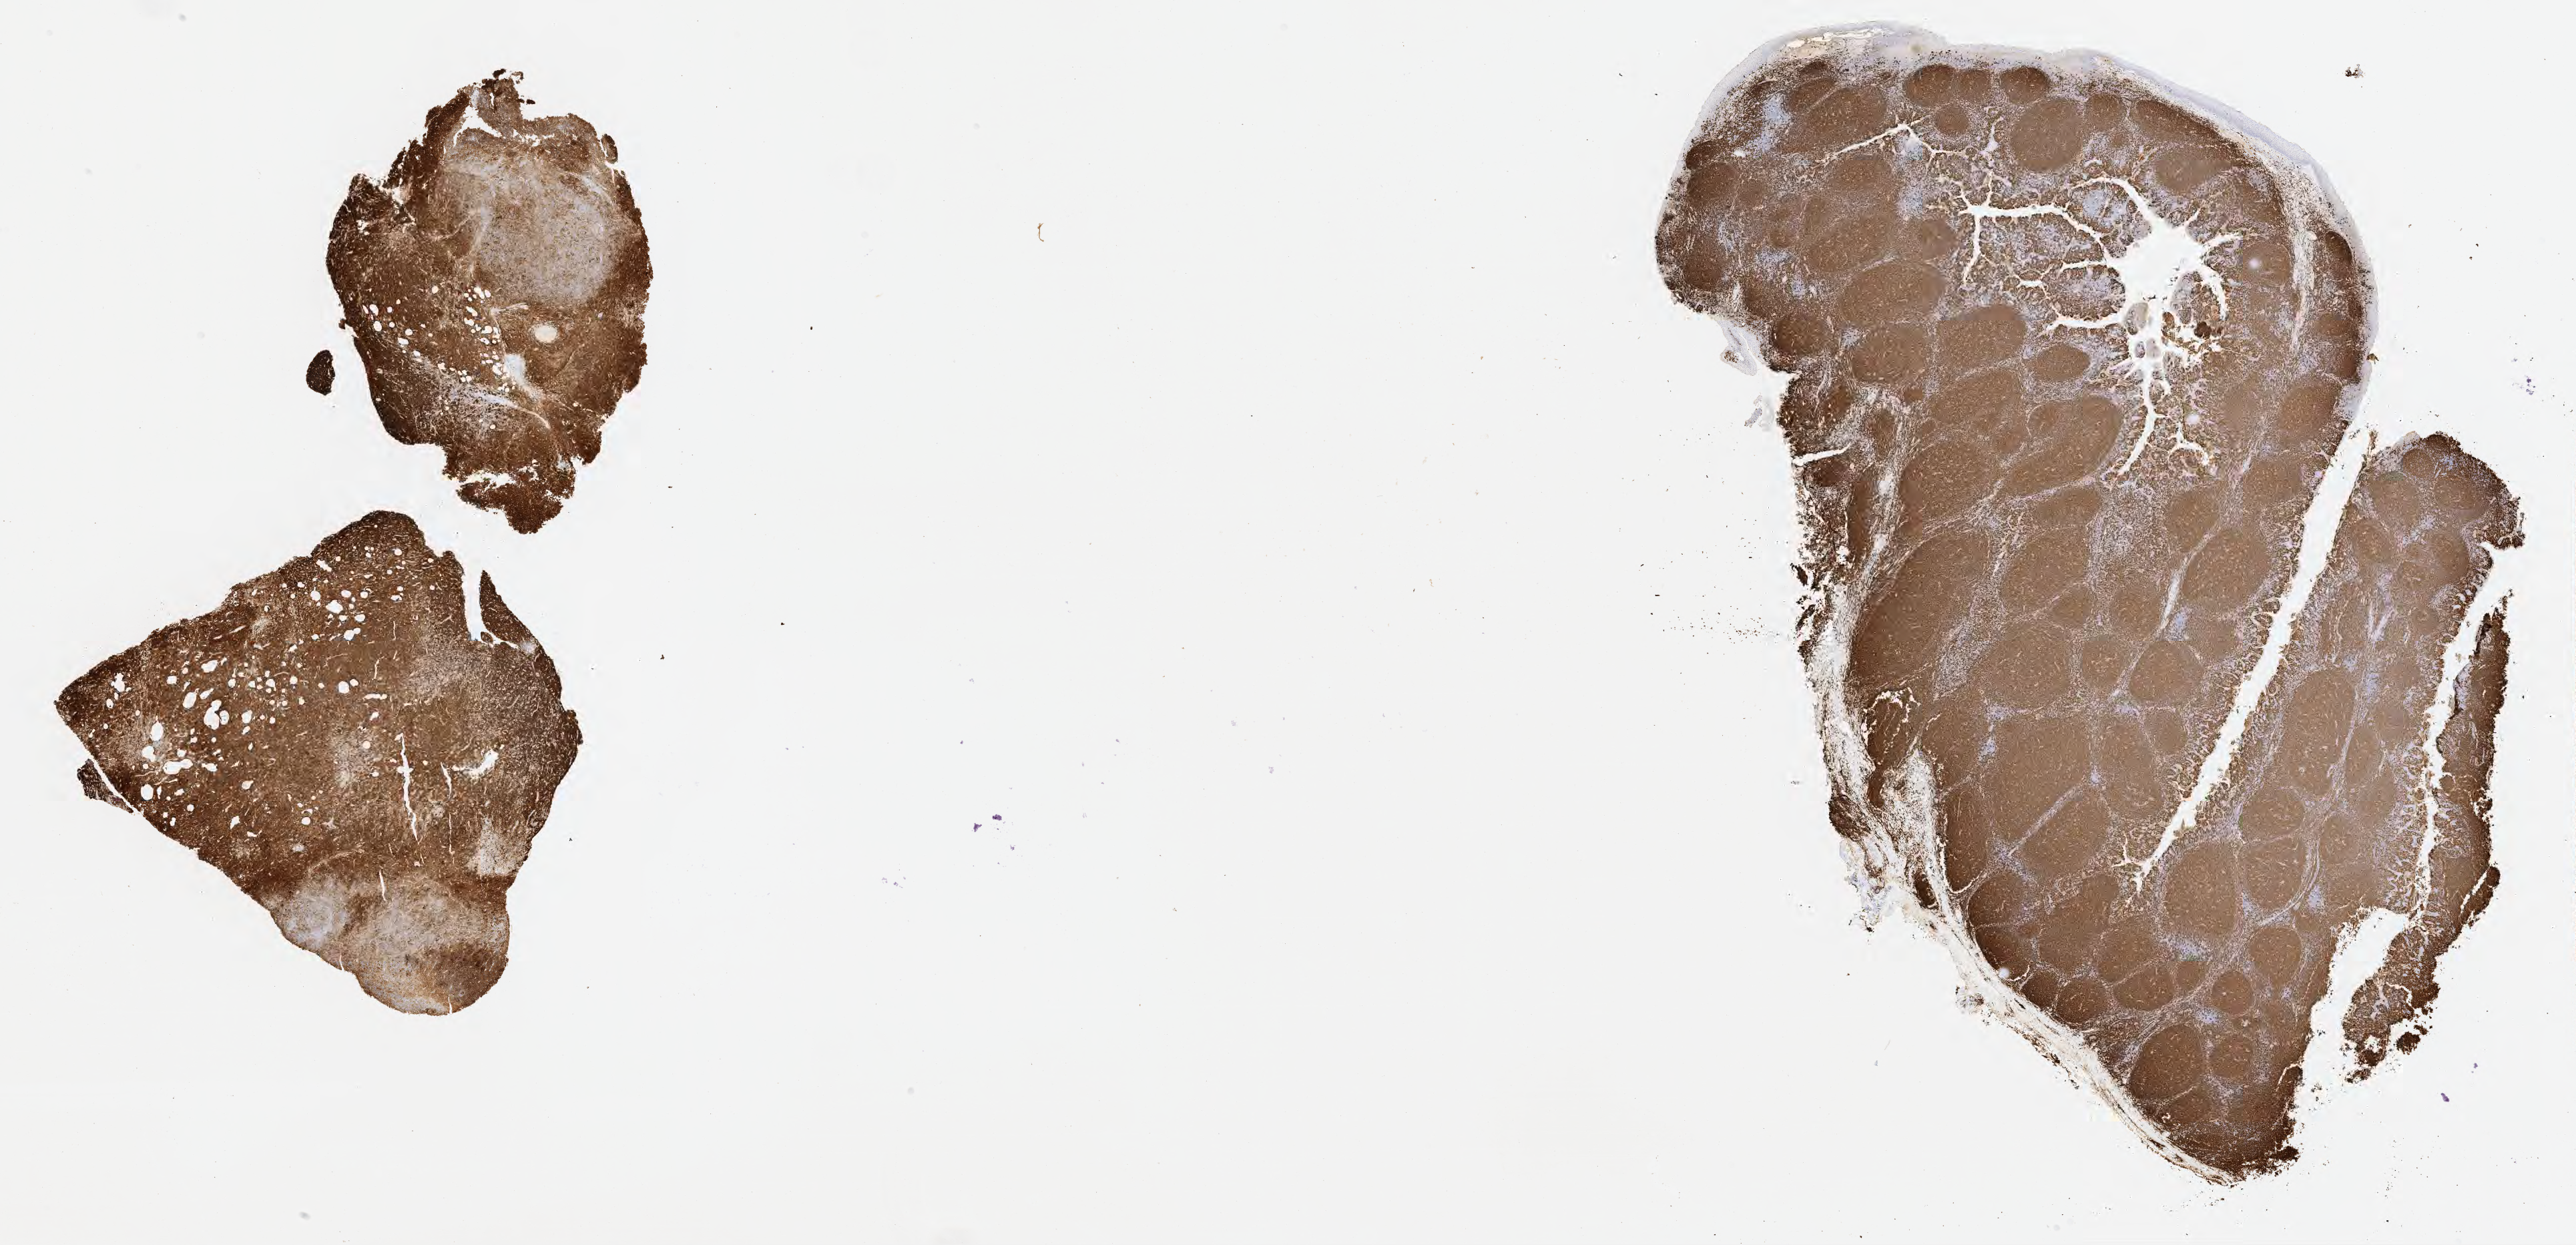
IHC for CD20, whole-slide image, a low-resolution overview of the entire scanned area, about 31.2 x 15.1 mm, tumor tissue, site: mandible. Male patient; age at initial diagnosis 7 years.
Diagnosis: Burkitt lymphoma, NOS.